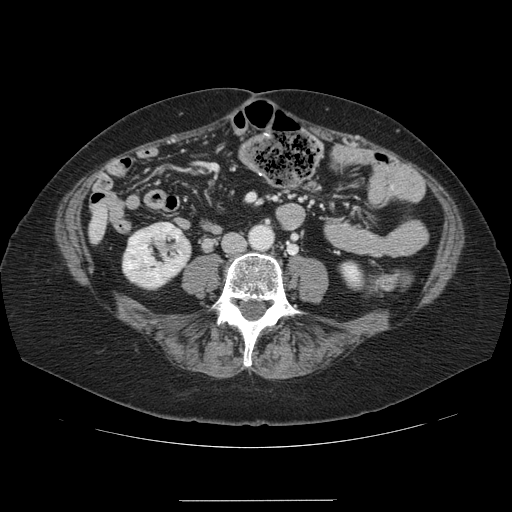
Contrast-enhanced abdominal CT, one axial slice; position 10 of 141 along the scan axis; intravenous contrast given; soft-tissue window (W 400 / L 40 HU); 2.5 mm slice thickness; 512 × 512 image matrix, field of view 393 × 393 mm. Female patient, age 74 years. Case-level facts recorded for this patient, not image findings: diagnosis: colorectal cancer liver metastases, imaged before liver resection; multiple liver metastases: yes.
Annotated regions visible in this slice (expert manual segmentation):
- liver: bounding box (x1, y1, x2, y2) in pixels: (91, 210, 106, 240)
- planned liver remnant (the part of the liver to remain after resection): (96, 210, 106, 239)